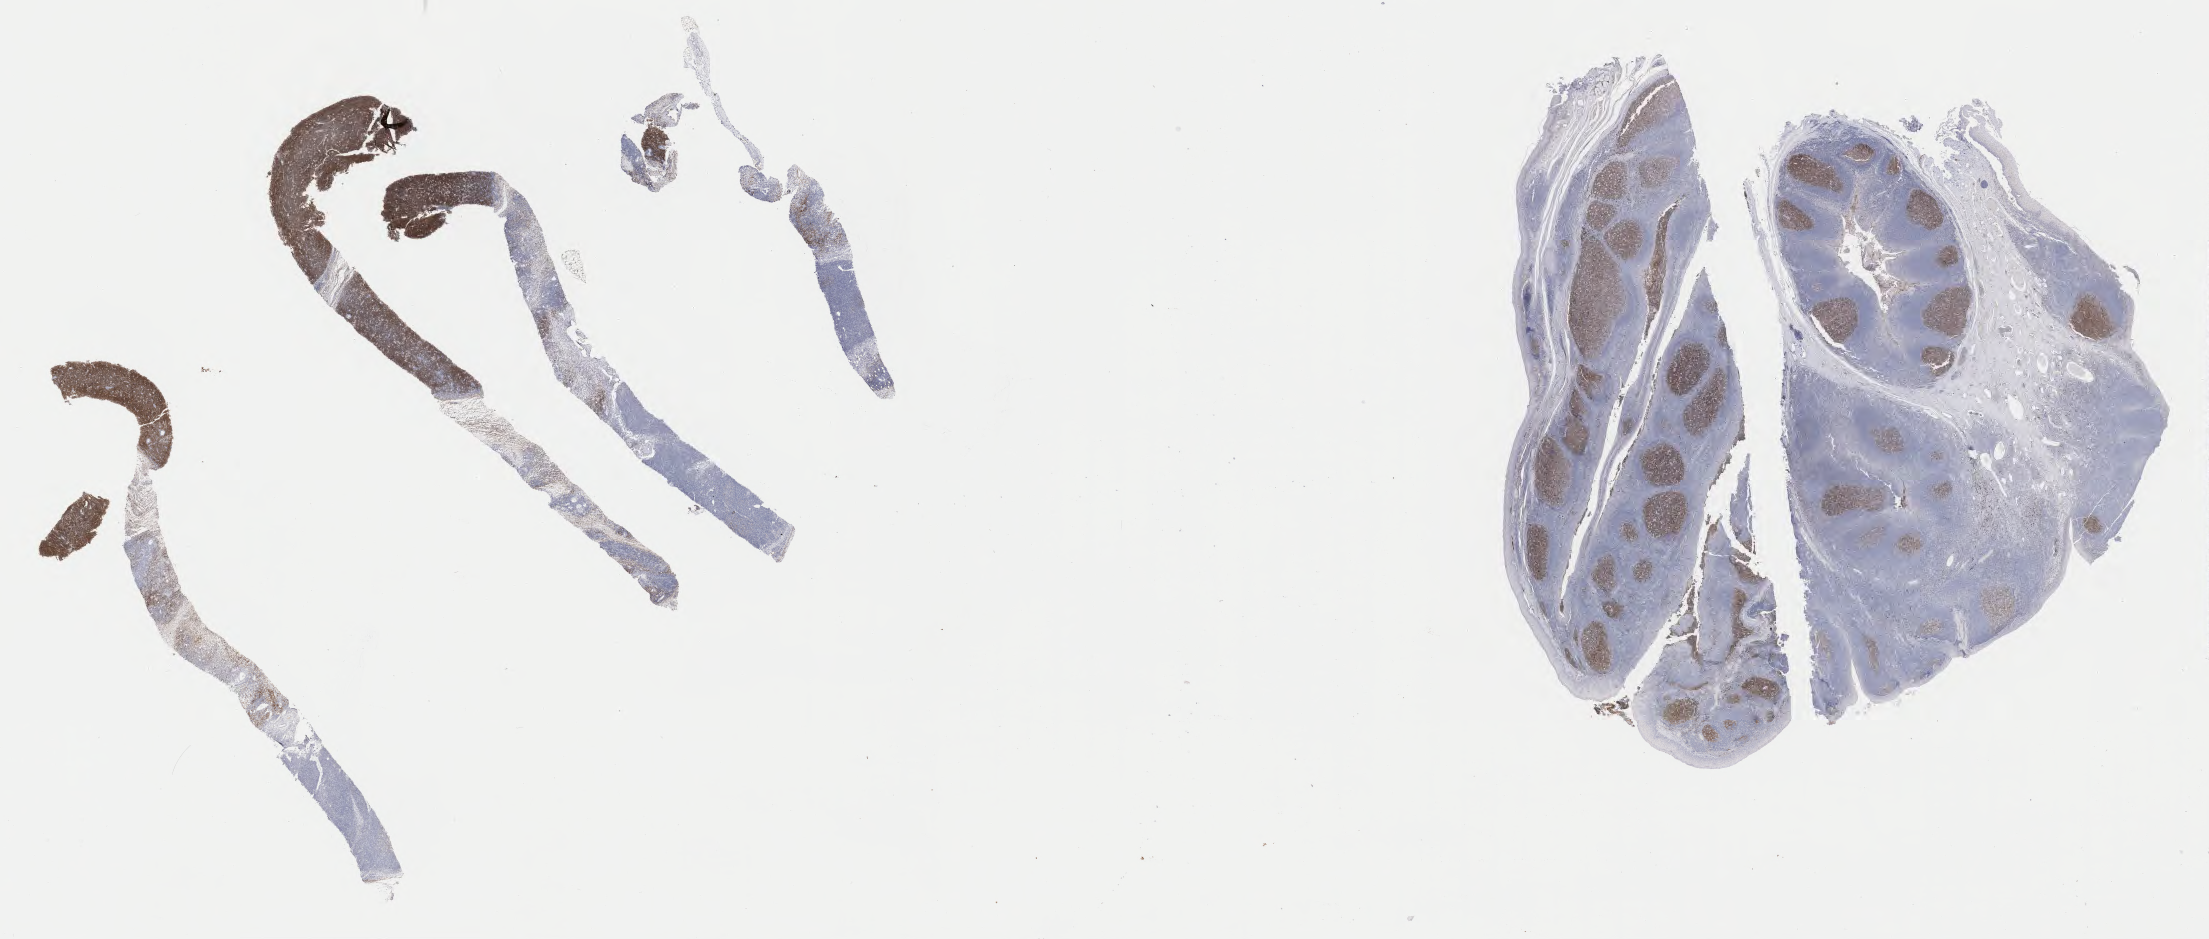
Whole-slide image, immunohistochemical stain for CD10 — a low-resolution overview of the entire scanned area, about 35.7 x 15.2 mm, tumor tissue. Patient: male, 47 years old.
Diagnosis: Burkitt lymphoma, NOS.